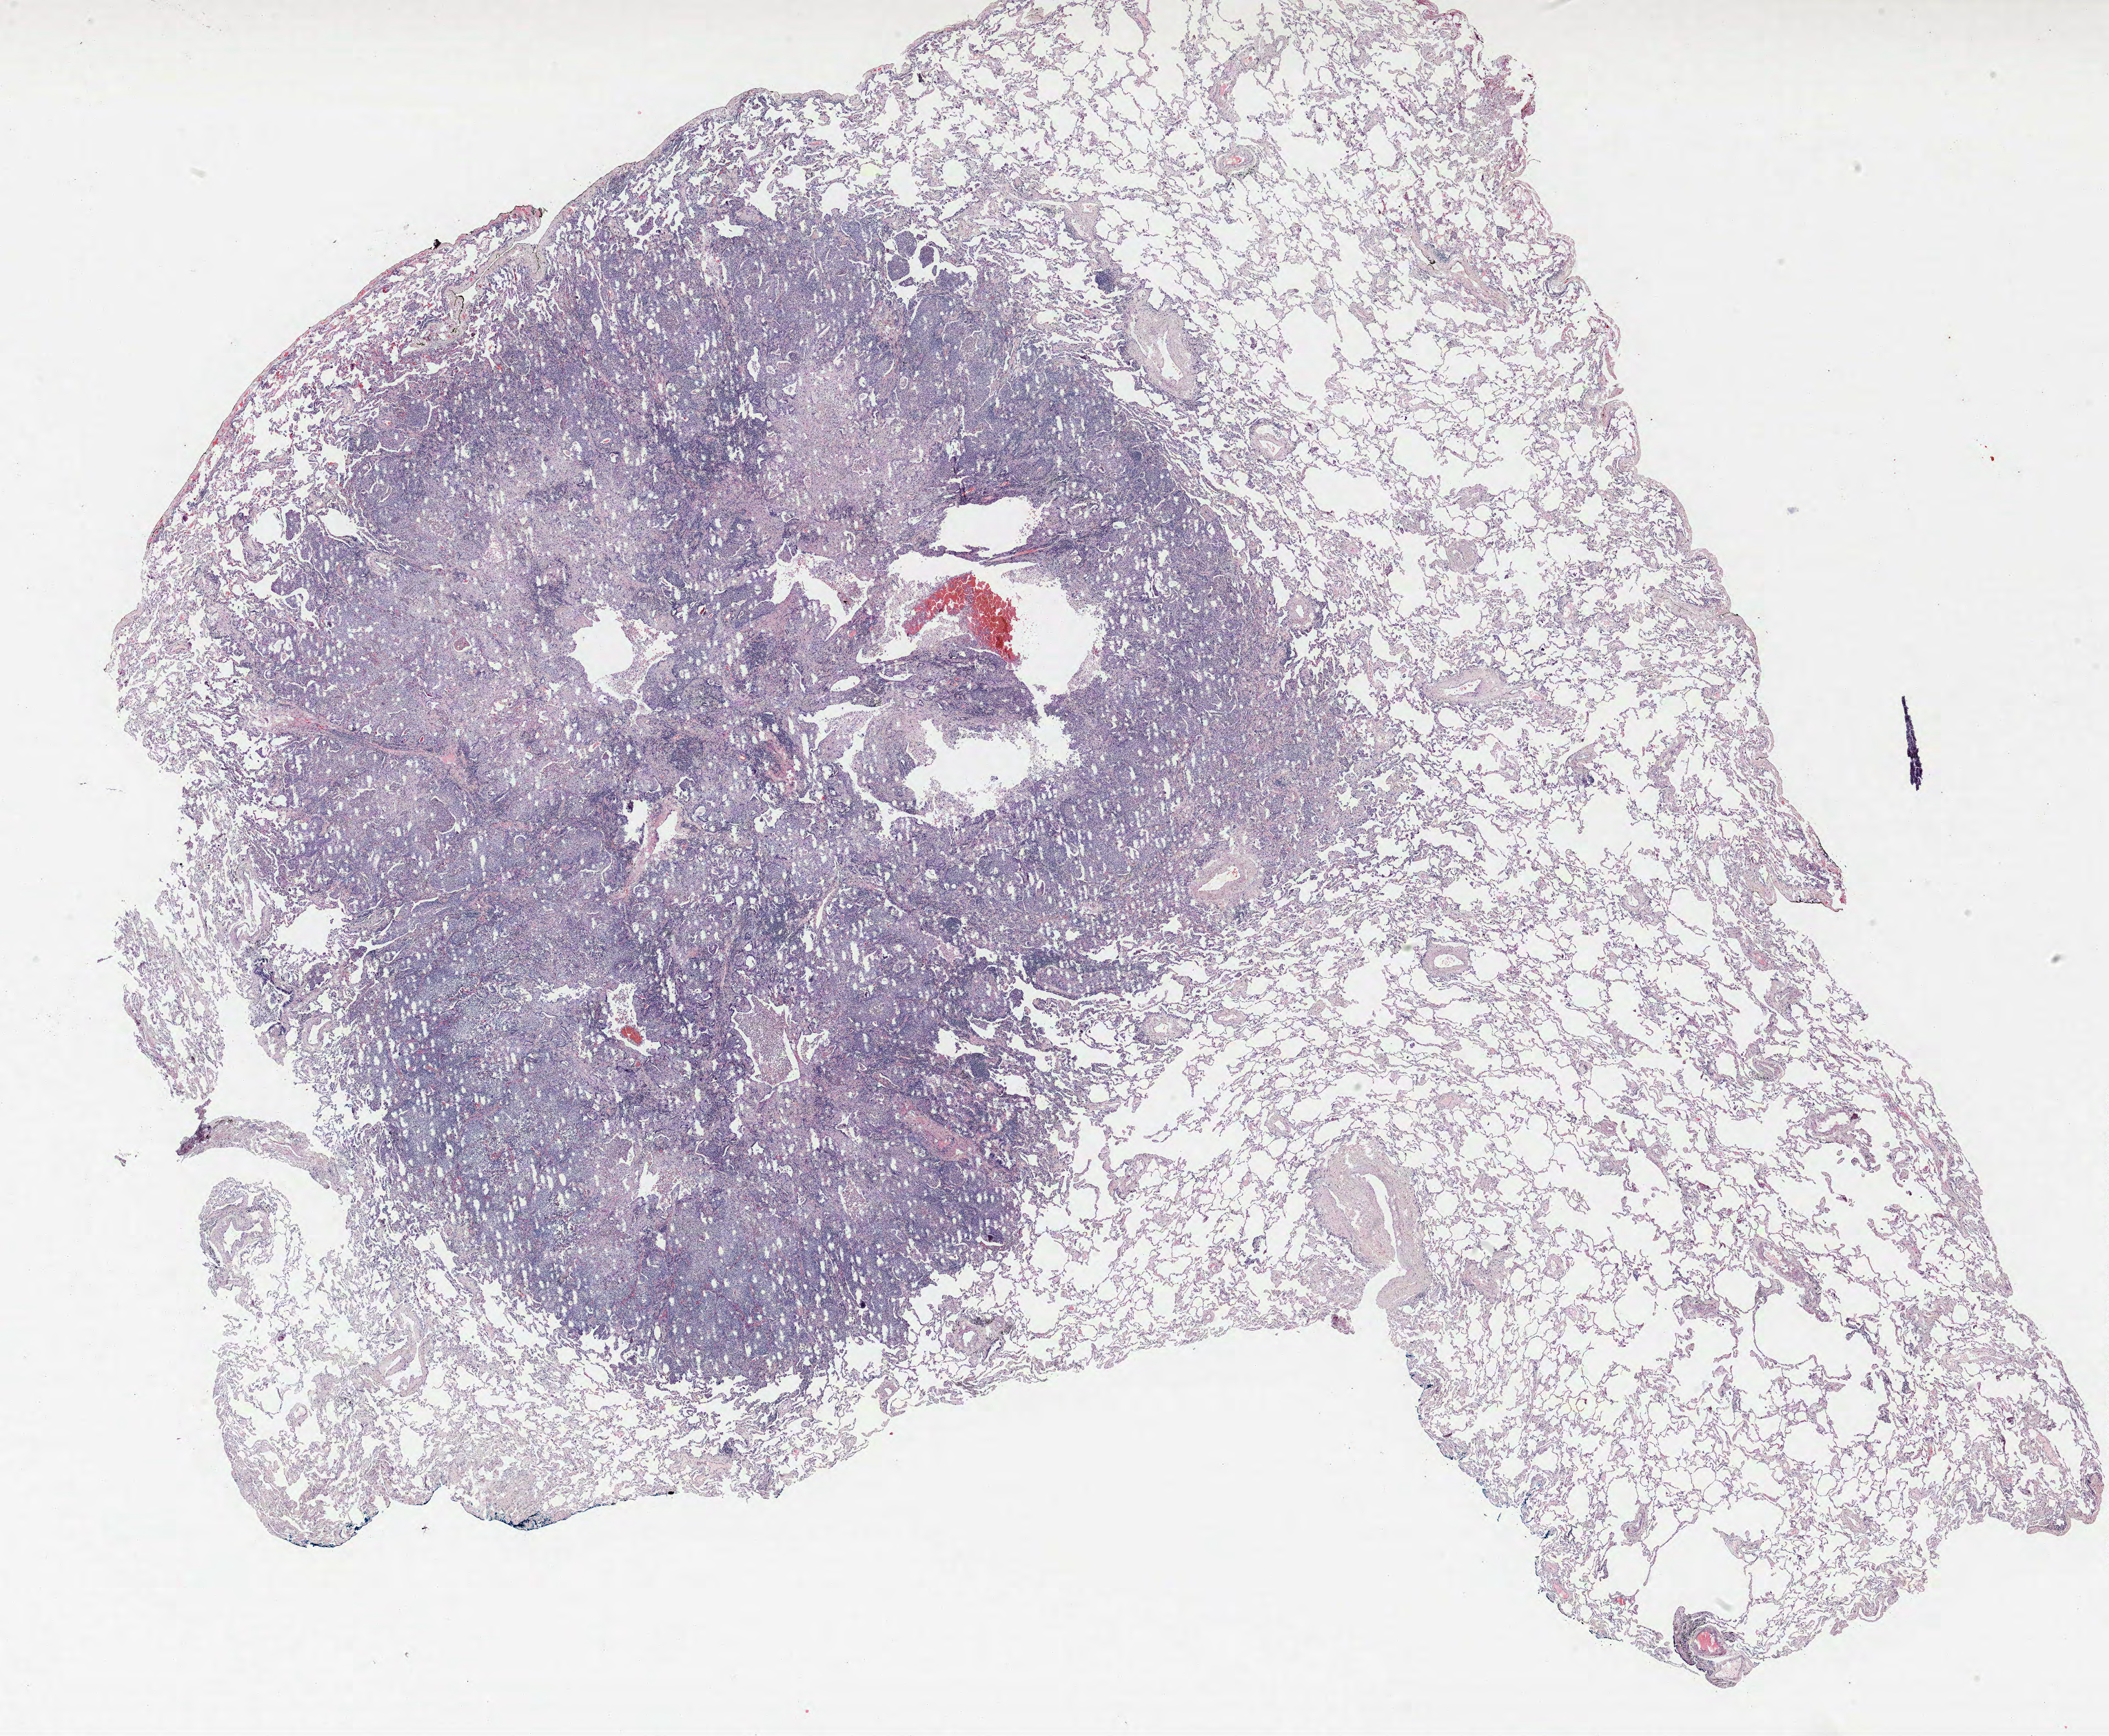
Whole-slide histology image, H&E-stained, a low-resolution overview of the entire scanned area, about 24.5 x 20.2 mm (from a 40x scan), FFPE section, lung. Male, age 67 at enrolment. Grade: moderately differentiated (G2).
Tumour size (pathology): 15 mm. Primary tumour location (clinical record): left upper lobe. Participant's lung-cancer diagnosis: Squamous cell carcinoma, large cell, nonkeratinizing, NOS (ICD-O-3 8072/3). ICD-O-3 topography: upper lobe of lung (C34.1). Stage (AJCC 6th edition): IA.